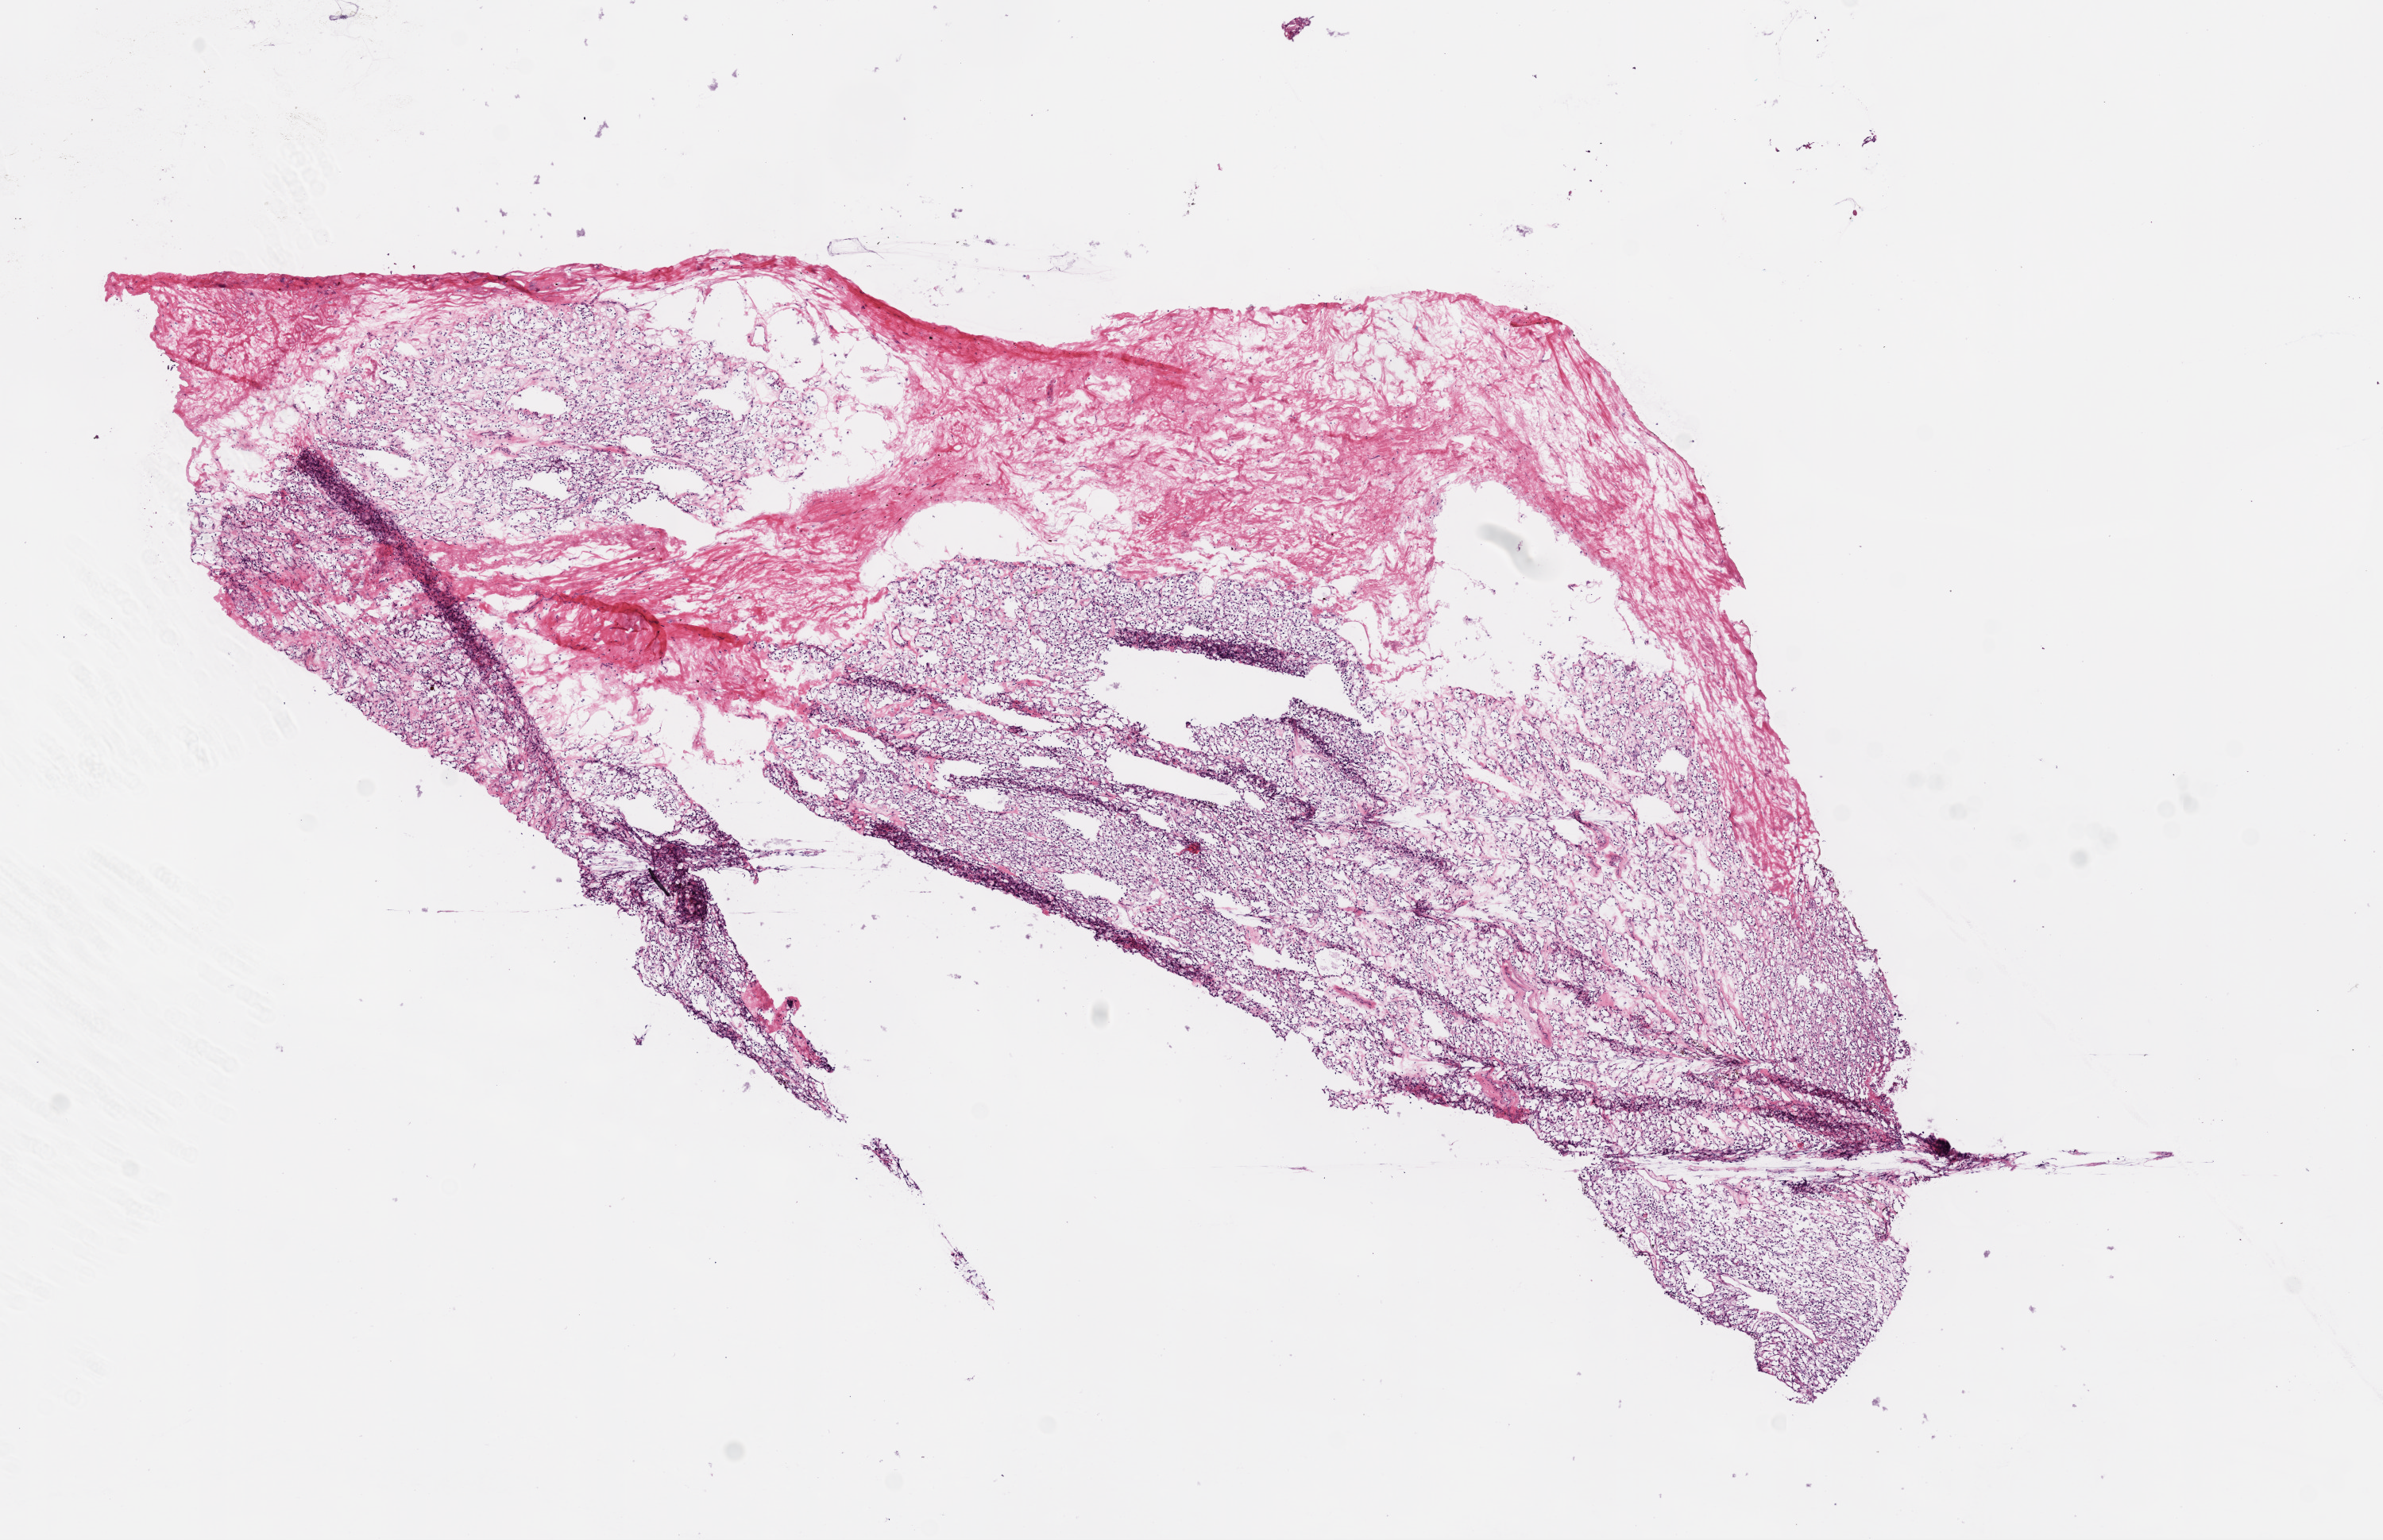
Hematoxylin and eosin (H&E) stained whole-slide image — a low-resolution overview of the entire scanned area, about 12.0 x 7.8 mm (acquisition: 20x scan). Frozen section from the bottom of the tissue portion. Primary tumour sample from the kidney. Male, age 54 years at initial diagnosis. Histologic grade: G2 (moderately differentiated). Composition of this section per pathologist review: tumour cells 70%, tumour nuclei 80%, normal cells 0%, stromal cells 30%, necrosis 0%.
- AJCC pathologic stage: I
- diagnosis: Clear cell adenocarcinoma, NOS